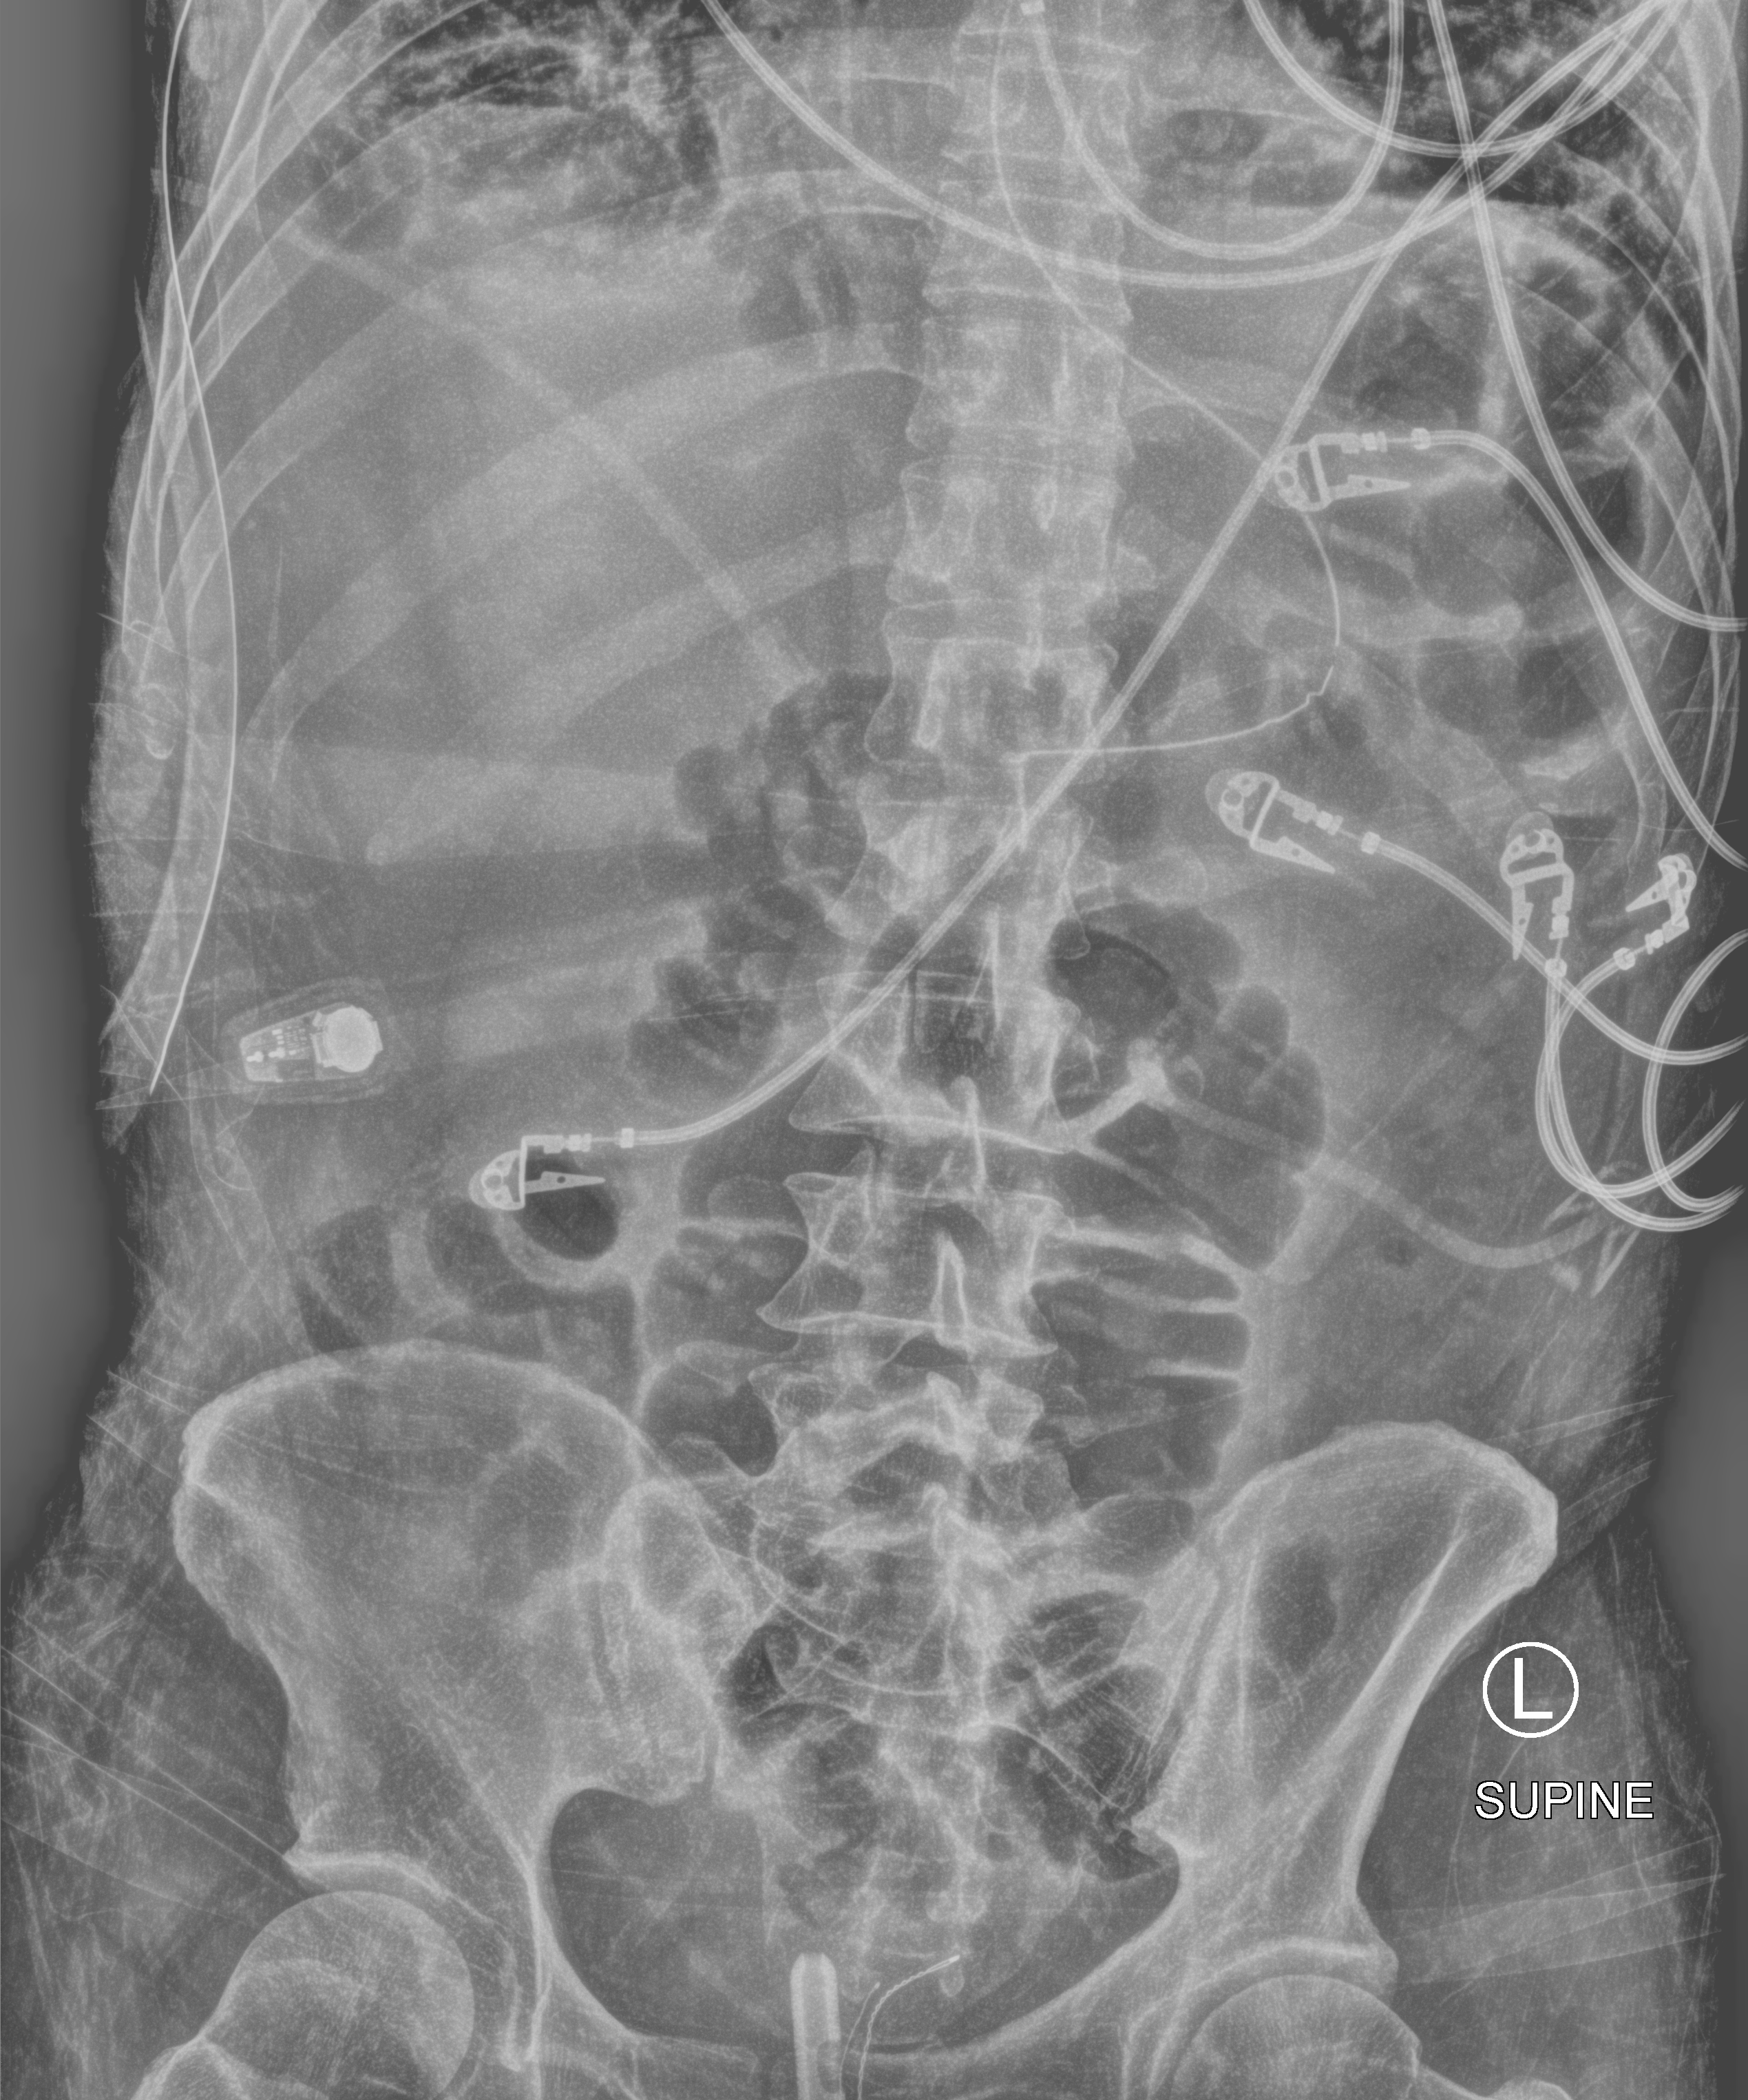
Portable abdomen radiograph, anteroposterior (AP) projection. Male patient hospitalised with COVID-19, age 18–59 years.
From the hospital-stay record, not from the radiograph (when in the stay this image was taken is not recorded):
- admitted to intensive care during this hospital stay: yes